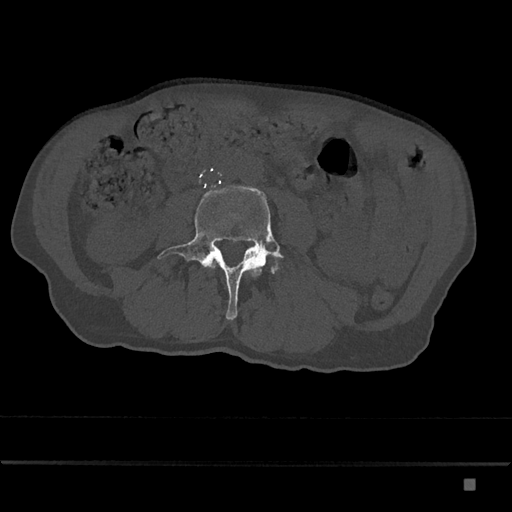
CT including the spine, one axial slice. 120 kVp. Bone window (W 1800 / L 400 HU). 0.5 mm slice thickness. 512 × 512 image matrix, field of view 390 × 390 mm. Patient: male, 72 years. Case-level facts recorded for this patient, not image findings: primary cancer: prostate.
Structures marked on this image (semi-automatic segmentation, software-assisted and operator-edited):
- L3 vertebra: bounding box (x1, y1, x2, y2) in pixels: (211, 258, 217, 266)
- L4 vertebra: (158, 185, 284, 320)